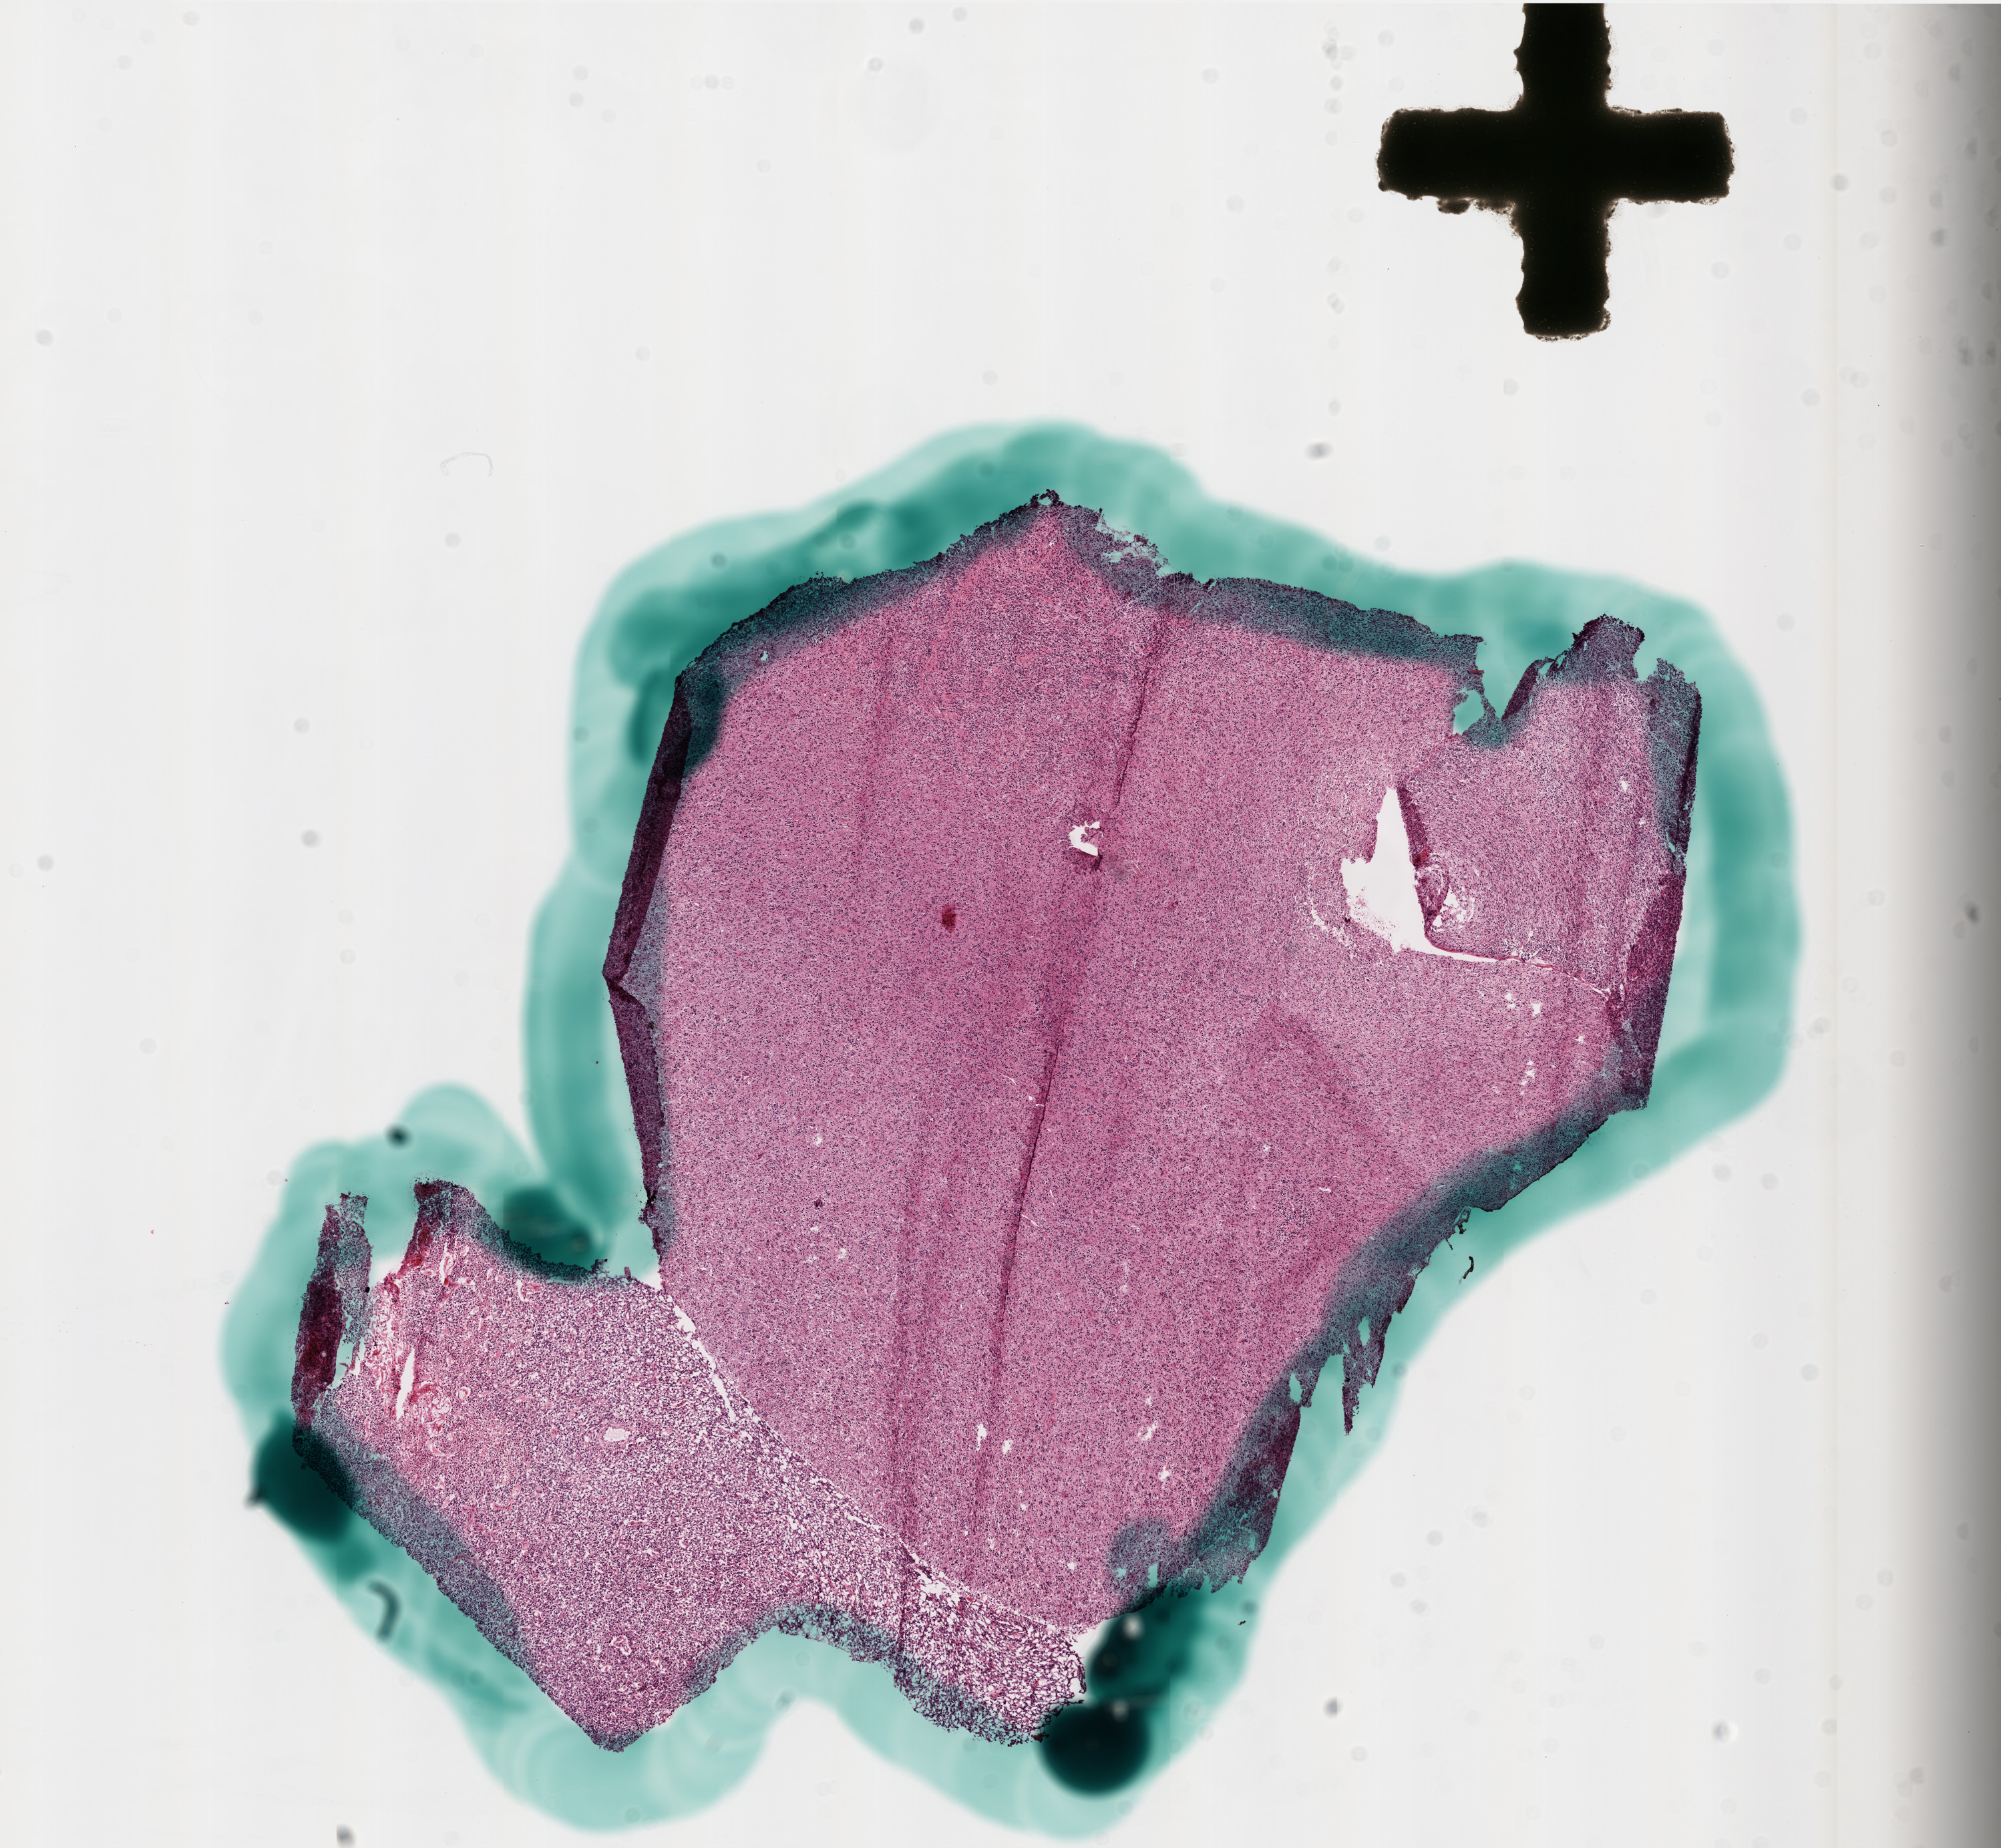
Digitized H&E tissue section (whole slide) — whole scanned area (about 12.0 x 11.1 mm) shown as a low-resolution overview; frozen section; primary tumour sample from the brain. Male, age 54 years at initial diagnosis. Slide review estimates, as recorded: tumour cells 95%, tumour nuclei 100%, normal cells 0%, stromal cells 0%, necrosis 5%.
• pathologic diagnosis: Glioblastoma